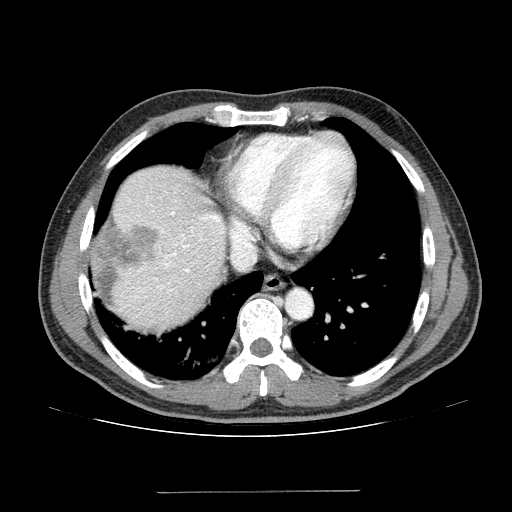
Contrast-enhanced abdominal CT (liver protocol), one axial slice; reconstruction kernel STANDARD; 100 kVp; one of 2 acquisitions stored at this slice position; soft-tissue window (W 400 / L 40 HU); 2.5 mm slice thickness; 512 × 512 image matrix, field of view 380 × 380 mm. Case-level facts recorded for this patient, not image findings: diagnosis: hepatocellular carcinoma (patient treated with transarterial chemoembolisation; whether this scan precedes or follows treatment is not stated here); TNM stage (as recorded): Stage-I; Child-Pugh class: A; tumour nodularity: uninodular; tumour size: 10.3 cm.
Structures marked on this image (semi-automatically segmented with operator editing):
- liver parenchyma outside the tumour (the mass and vessels are separate outlines, so this box may not span the whole liver): box from (x=90, y=166) to (x=226, y=328) px
- mass: (x=87, y=221)–(x=157, y=273)
- liver vessels: (x=129, y=200)–(x=223, y=298)